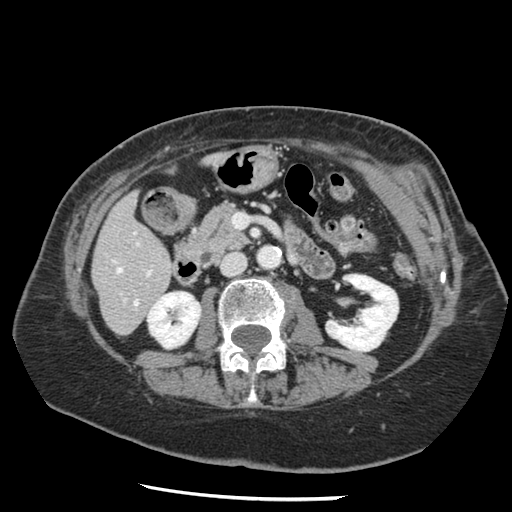
Contrast-enhanced abdominal CT, one axial slice. Position 50 of 148 along the scan axis. Reconstruction kernel STANDARD. 120 kVp. Intravenous contrast given. Soft-tissue window (W 400 / L 40 HU). 512 × 512 image matrix, field of view 330 × 330 mm. Female patient, age 85 years. Case-level facts recorded for this patient, not image findings: diagnosis: colorectal cancer liver metastases, imaged before liver resection; multiple liver metastases: no; largest metastasis: 0.9 cm; chemotherapy before resection: yes.
Structures marked on this image (expert manual segmentation):
- hepatic veins: bounding box <116,268,138,305> (left, top, right, bottom; pixels)
- liver: <93,159,213,334>
- planned liver remnant (the part of the liver to remain after resection): <94,159,213,331>